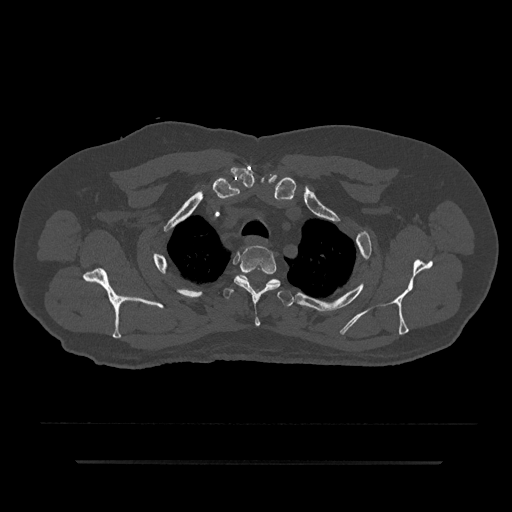
CT including the spine, one axial slice. Slice 687 of 797 in the series (ordered by position). 120 kVp. Bone window (W 1800 / L 400 HU). 0.5 mm slice thickness. 512 × 512 image matrix, field of view 464 × 464 mm. Patient: male, 59 years. Case-level facts recorded for this patient, not image findings: primary cancer: bile ducts.
Structures marked on this image (semi-automatic segmentation, software-assisted and operator-edited):
- T2 vertebra: bounding box [x1, y1, x2, y2] px = [234, 246, 281, 326]
- T3 vertebra: [224, 288, 293, 307]